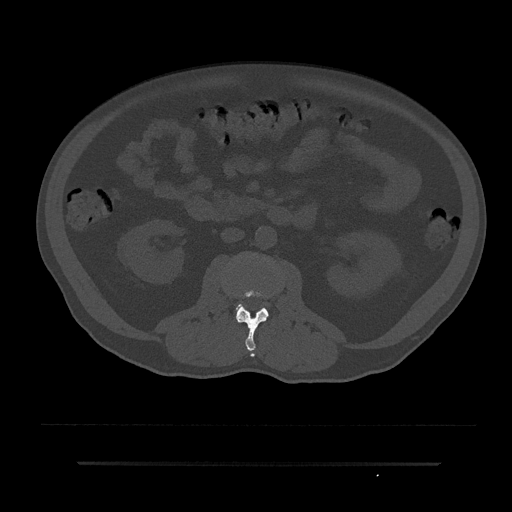
CT including the spine, one axial slice. Position 48 of 797 along the scan axis. Reconstruction kernel Br40s/3. 120 kVp. Bone window (W 1800 / L 400 HU). 512 × 512 image matrix, field of view 464 × 464 mm. Male patient, age 59 years. Case-level facts recorded for this patient, not image findings: primary cancer: bile ducts.
Annotated regions visible in this slice (semi-automatic segmentation, software-assisted and operator-edited):
- L2 vertebra: bounding box [x1, y1, x2, y2] px = [236, 278, 277, 357]